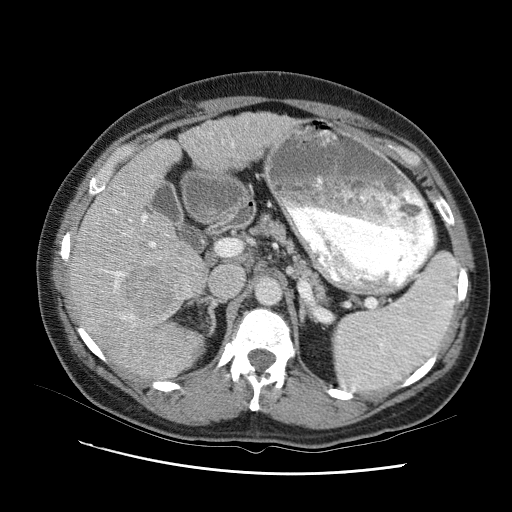
Contrast-enhanced abdominal CT (liver protocol), one axial slice. Position 55 of 95 along the scan axis. Reconstruction kernel STANDARD. One of 2 acquisitions stored at this slice position. Soft-tissue window (W 400 / L 40 HU). 2.5 mm slice thickness. 512 × 512 image matrix, field of view 360 × 360 mm. From the clinical record (not read from this slice): diagnosis: hepatocellular carcinoma (patient treated with transarterial chemoembolisation; whether this scan precedes or follows treatment is not stated here); TNM stage (as recorded): Stage-I; Child-Pugh class: B; tumour differentiation: moderately differentiated; tumour nodularity: uninodular.
Outlined on this slice (semi-automatically segmented with operator editing):
- liver parenchyma outside the tumour (the mass and vessels are separate outlines, so this box may not span the whole liver): bounding box [x1, y1, x2, y2] px = [66, 106, 298, 378]
- mass: [127, 263, 175, 308]
- liver vessels: [104, 132, 237, 359]